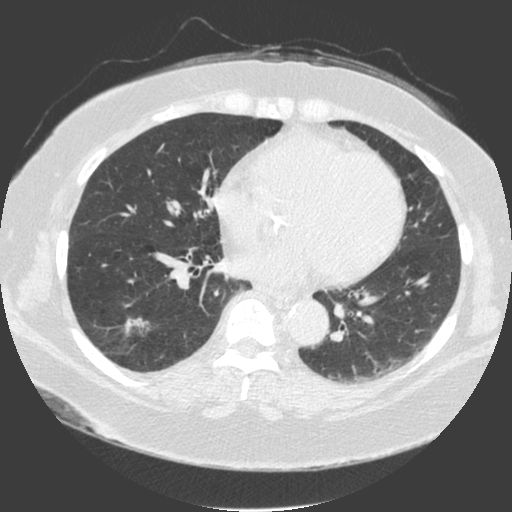
Low-dose screening chest CT, axial slice, third screening round (two years after baseline), lung window (W 1500 / L -600 HU), 2 mm slice thickness, 120 kVp, slice 96 of 175 in the series, 512 × 512 image matrix. Female, age 56 years at enrolment. Current smoker at enrolment.
Expert-annotated lung lesion, bounding box (x1, y1, x2, y2) in pixels: (110, 306, 160, 351). The screening reader recorded 4 non-calcified nodules or masses ≥4 mm on this exam (left lower lobe, right lower lobe, right lower lobe, right lower lobe); which of them this box marks is not recorded. Later outcome: lung cancer diagnosed 20 days after this screen — adenosquamous carcinoma, right lower lobe, poorly differentiated (G3), stage IA (AJCC 6th edition), 25 mm at pathology.